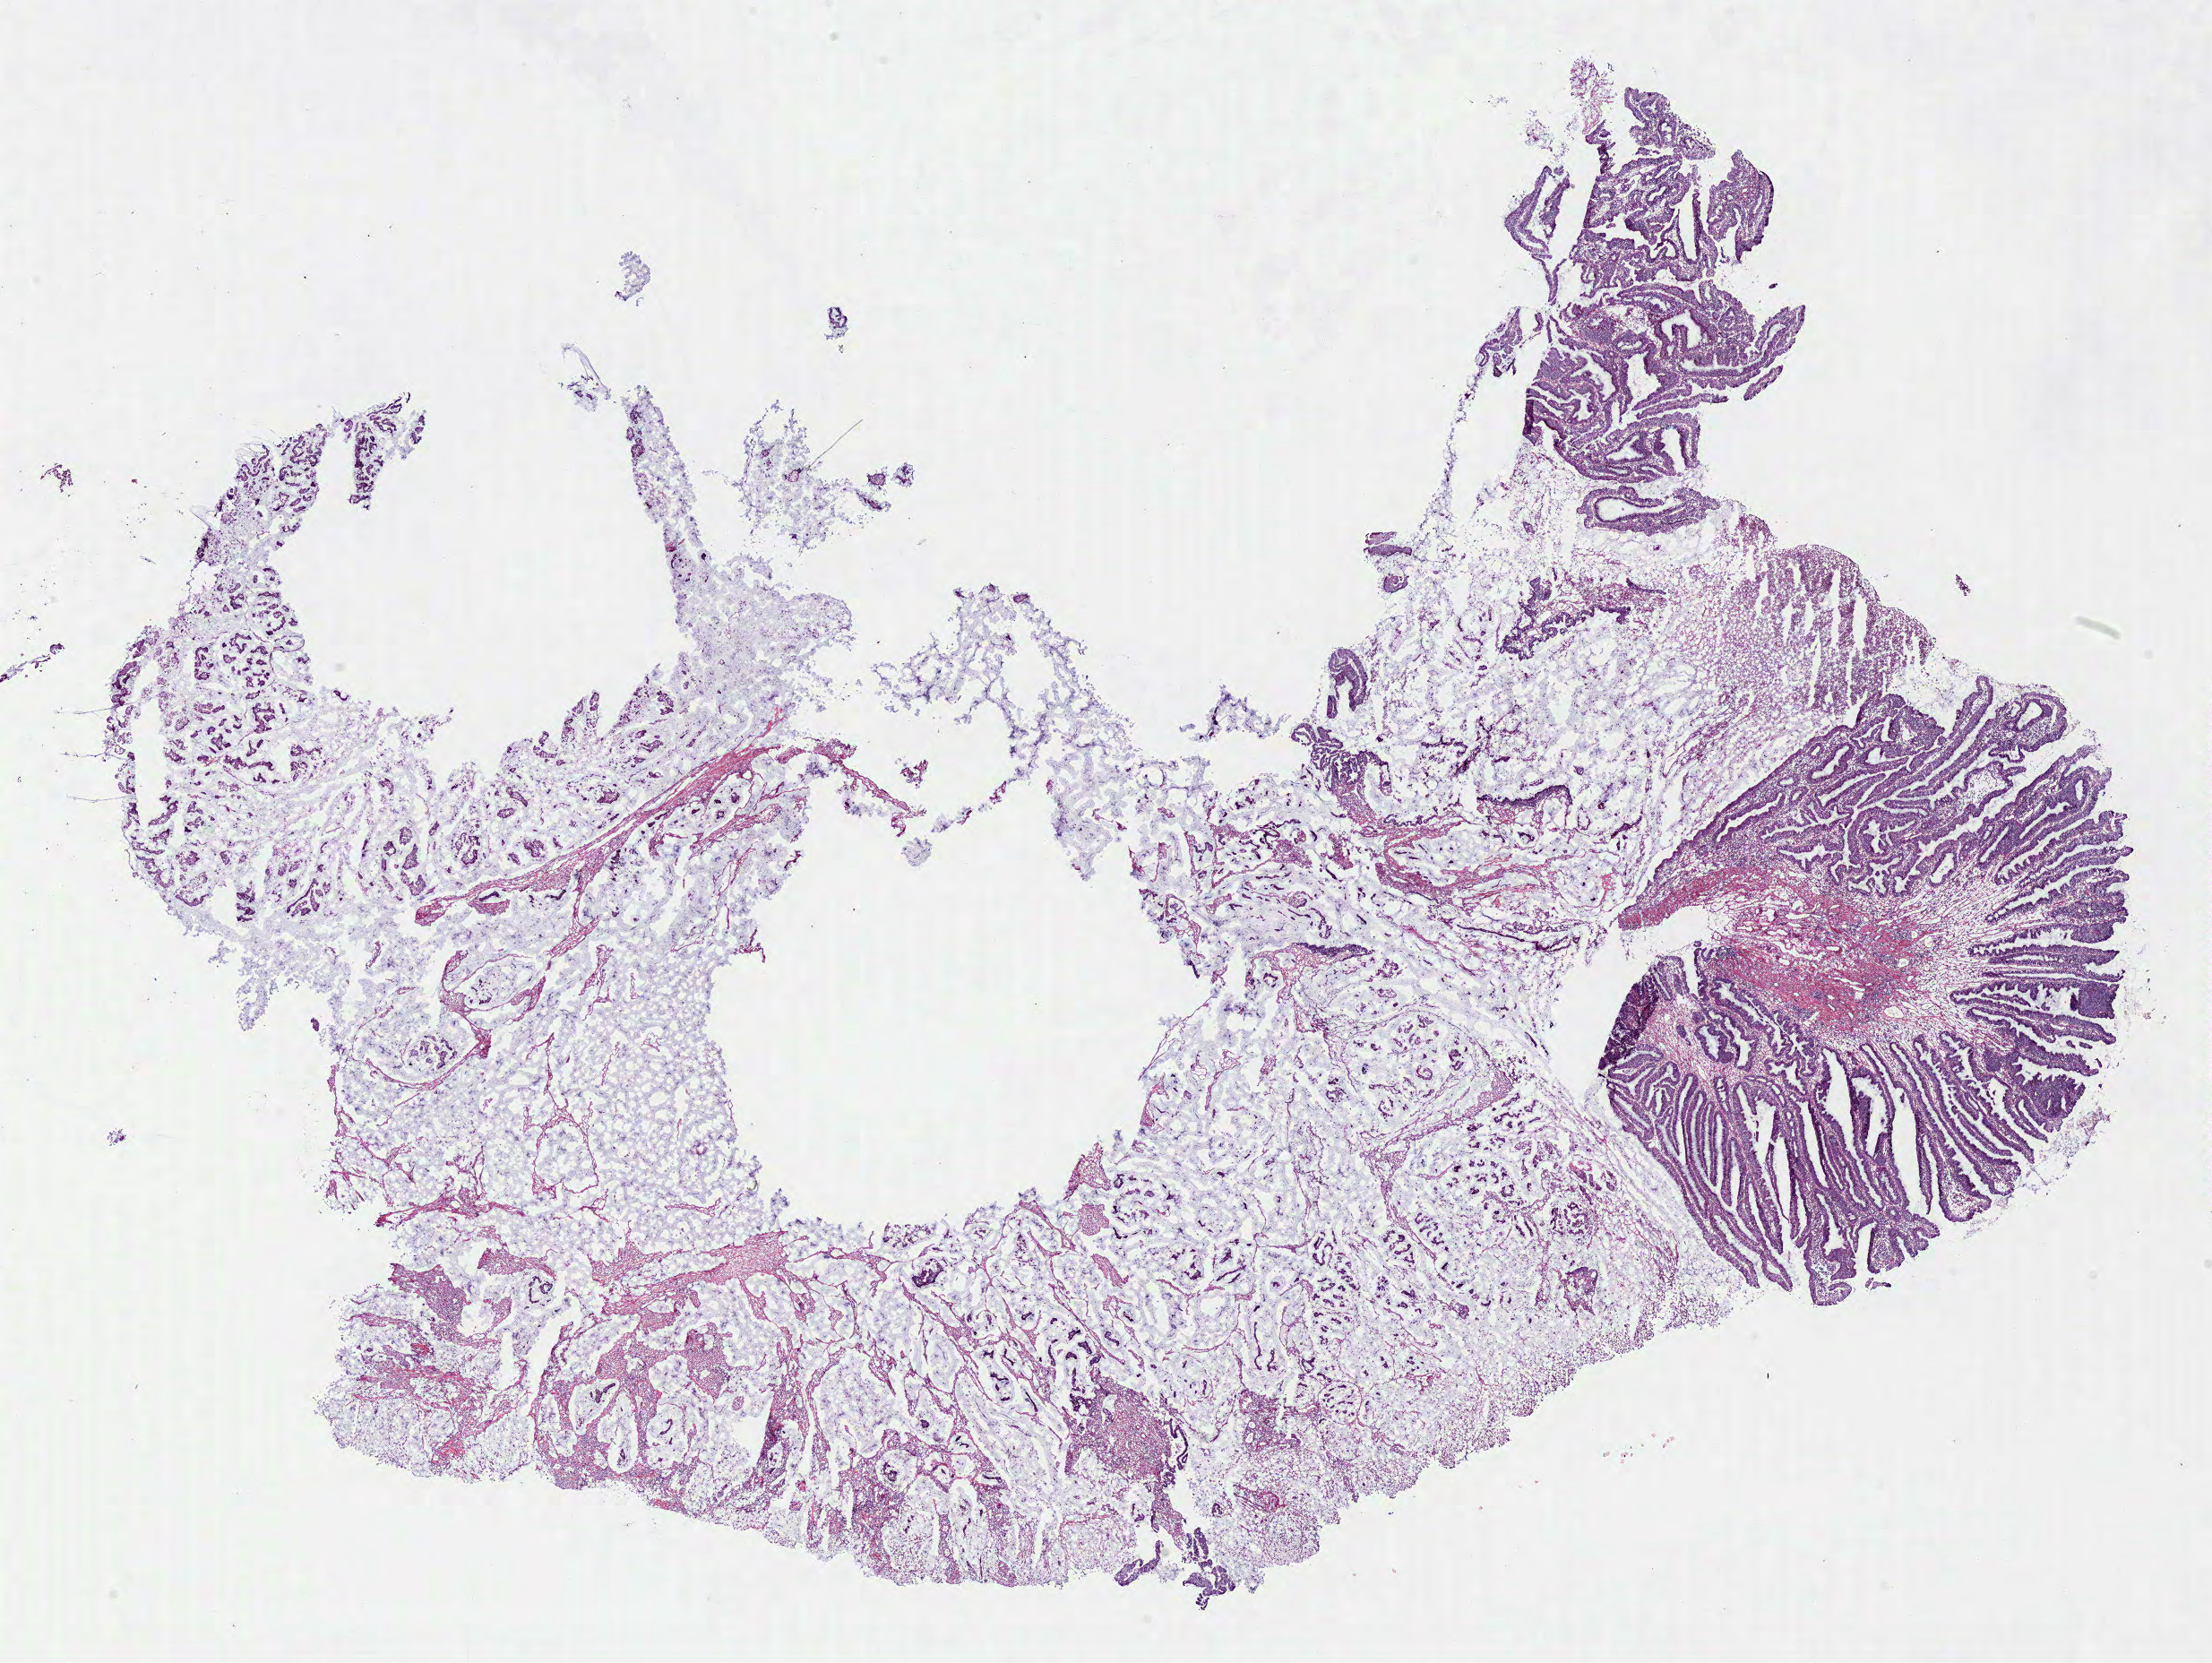
Whole-slide histology image, Hematoxylin and eosin (H&E) stained — whole scanned area (about 19.5 x 14.6 mm) shown as a low-resolution overview. Frozen section. Primary tumour sample from the colon. Female patient; age at initial diagnosis 60 years. Slide review estimates, as recorded: tumour cells 70%, tumour nuclei 50%.
Histologic diagnosis: Mucinous adenocarcinoma.